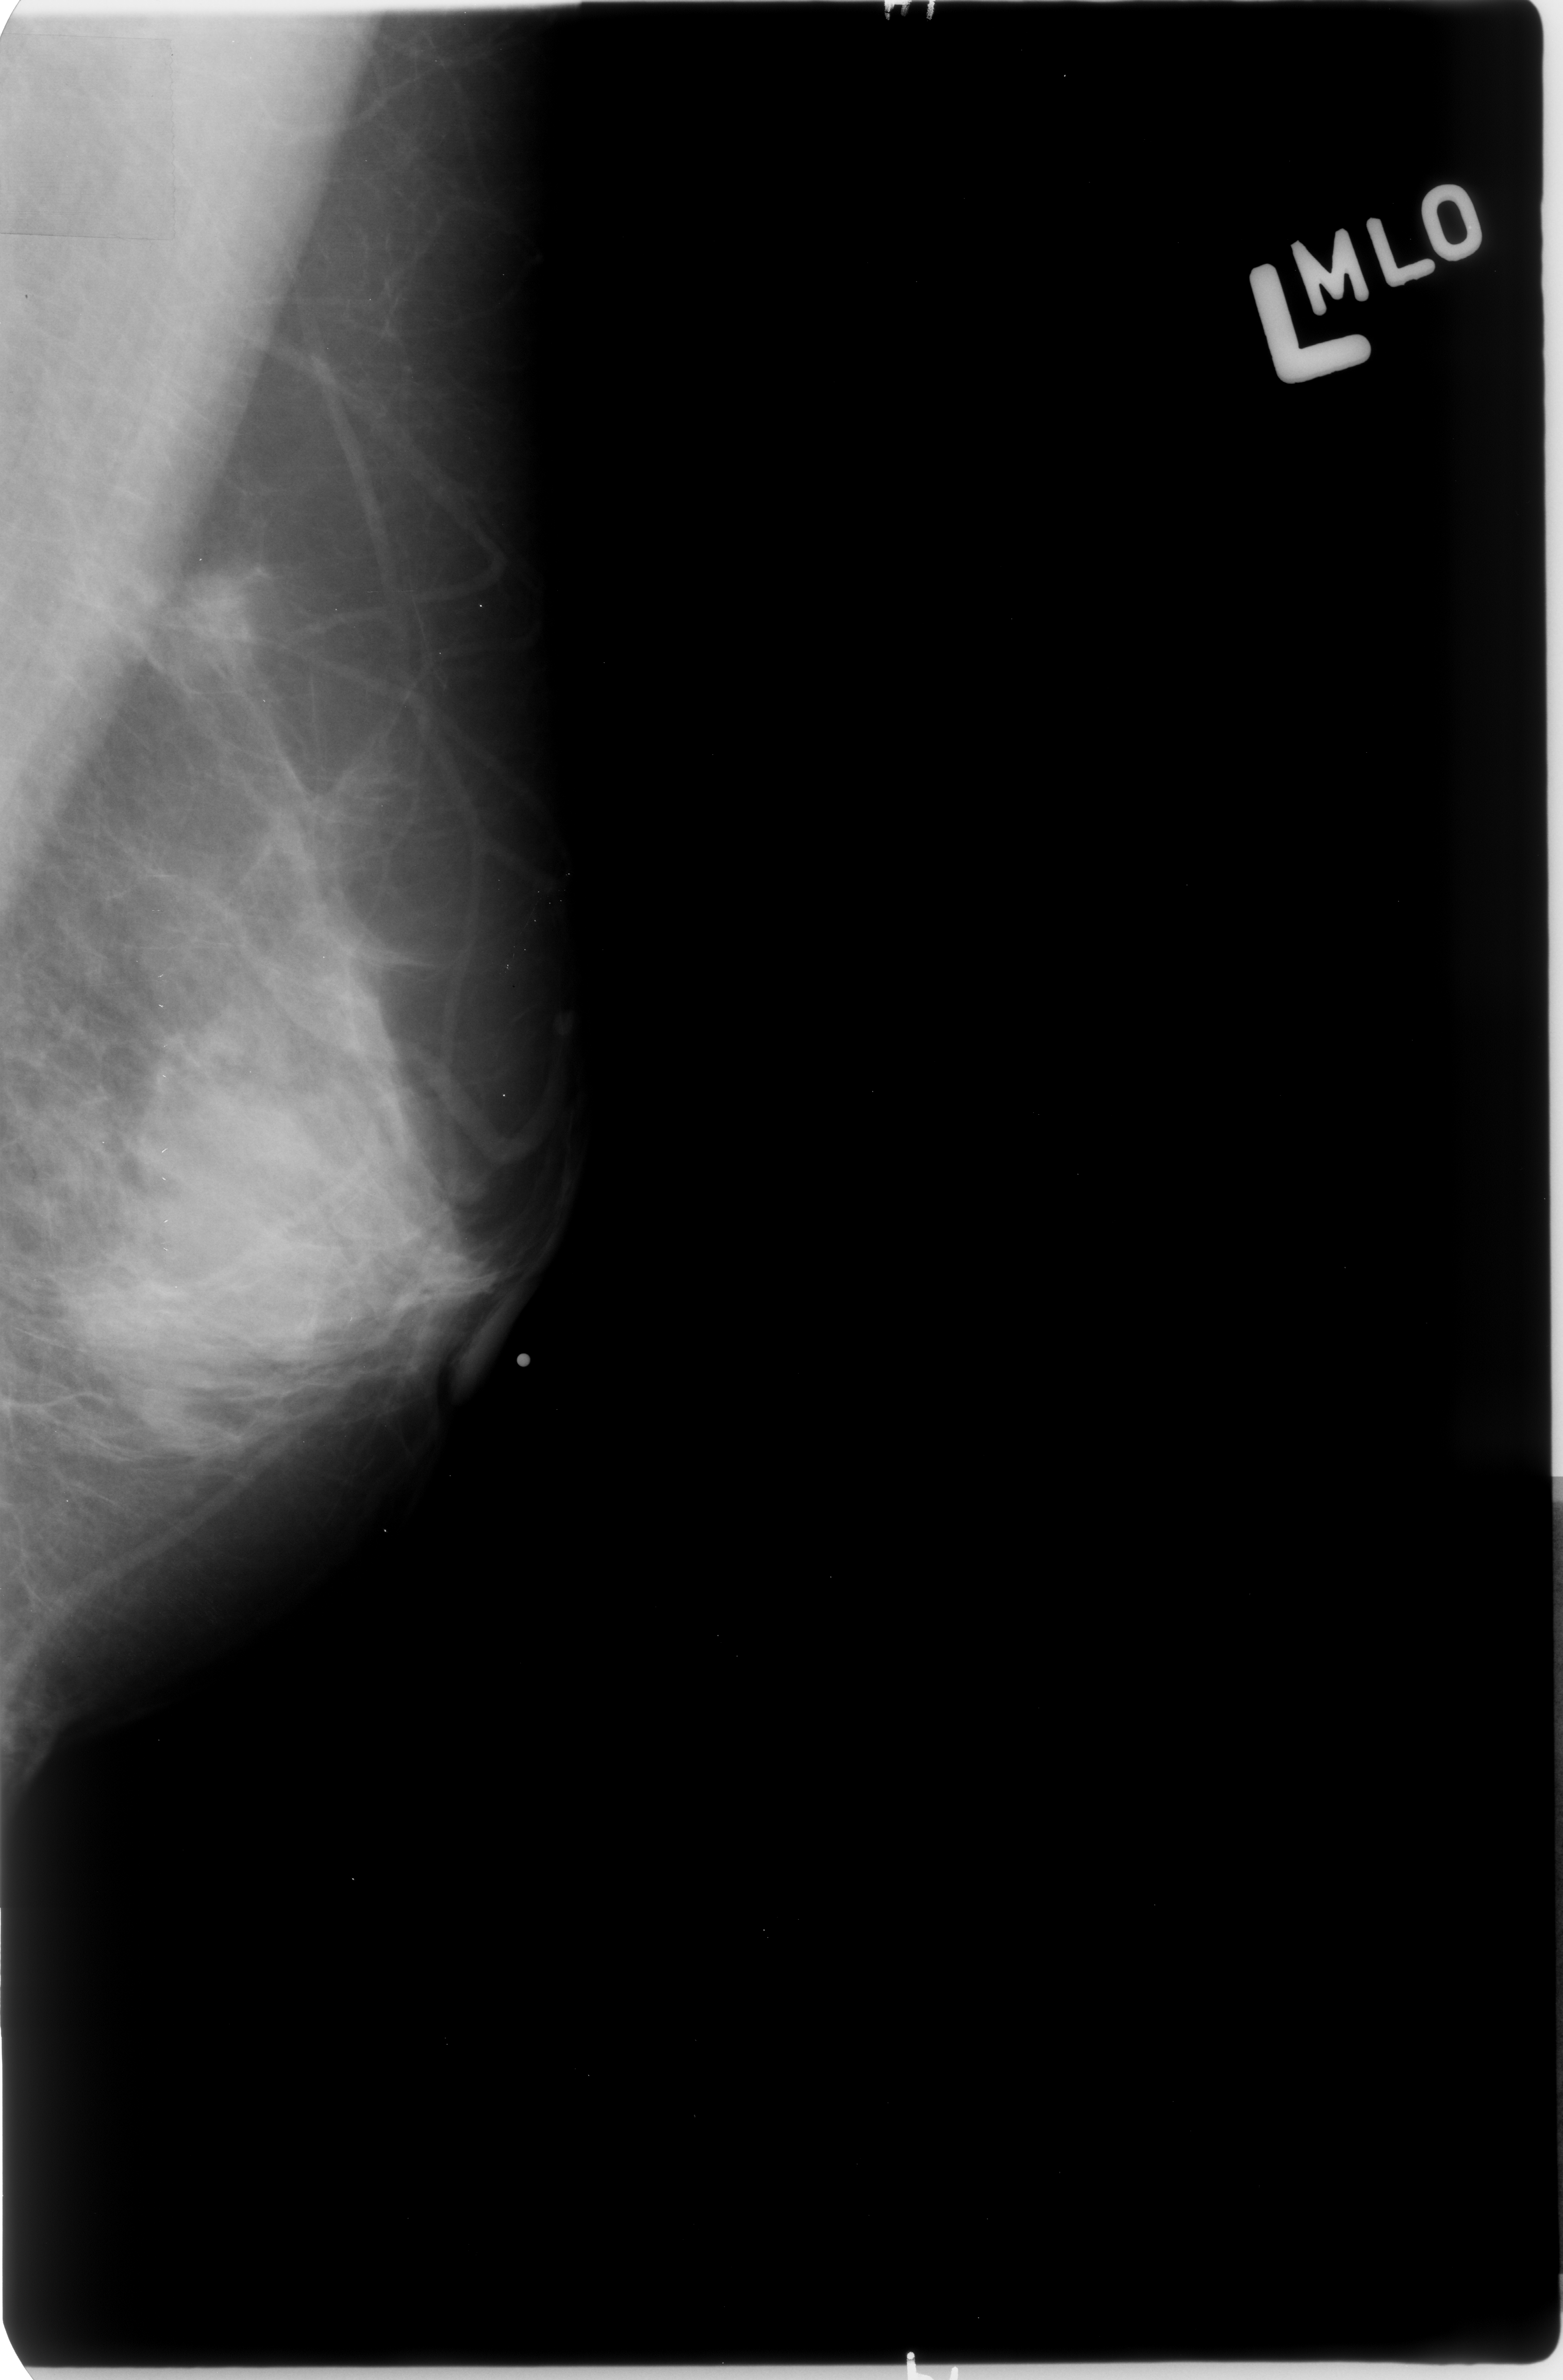
Mammogram (digitized film), left breast, mediolateral oblique (MLO) view, breast composition: heterogeneously dense (BI-RADS density category 3 of 4).
Marked abnormality: mass, shape irregular, margins ill defined / spiculated; BI-RADS assessment category 4; subtlety rating 4 on a 1 (subtle) to 5 (obvious) scale; pathology result (as recorded, not read from the image): malignant.